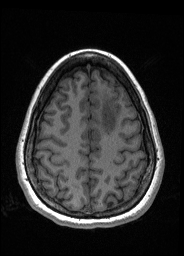
Pre-operative brain MRI before brain-tumour surgery, one axial slice; slice 55 of 176 in the series (ordered by position); T1-weighted post-contrast; 1 mm slice thickness; 184 × 256 image matrix. From the clinical record (not read from this slice): histopathology: Oligodendroglioma; WHO grade: 2; IDH mutation: yes; tumour location: Left Frontal.
Outlined on this slice (manually delineated by an expert):
- tumour: box from (x=99, y=95) to (x=118, y=134) px